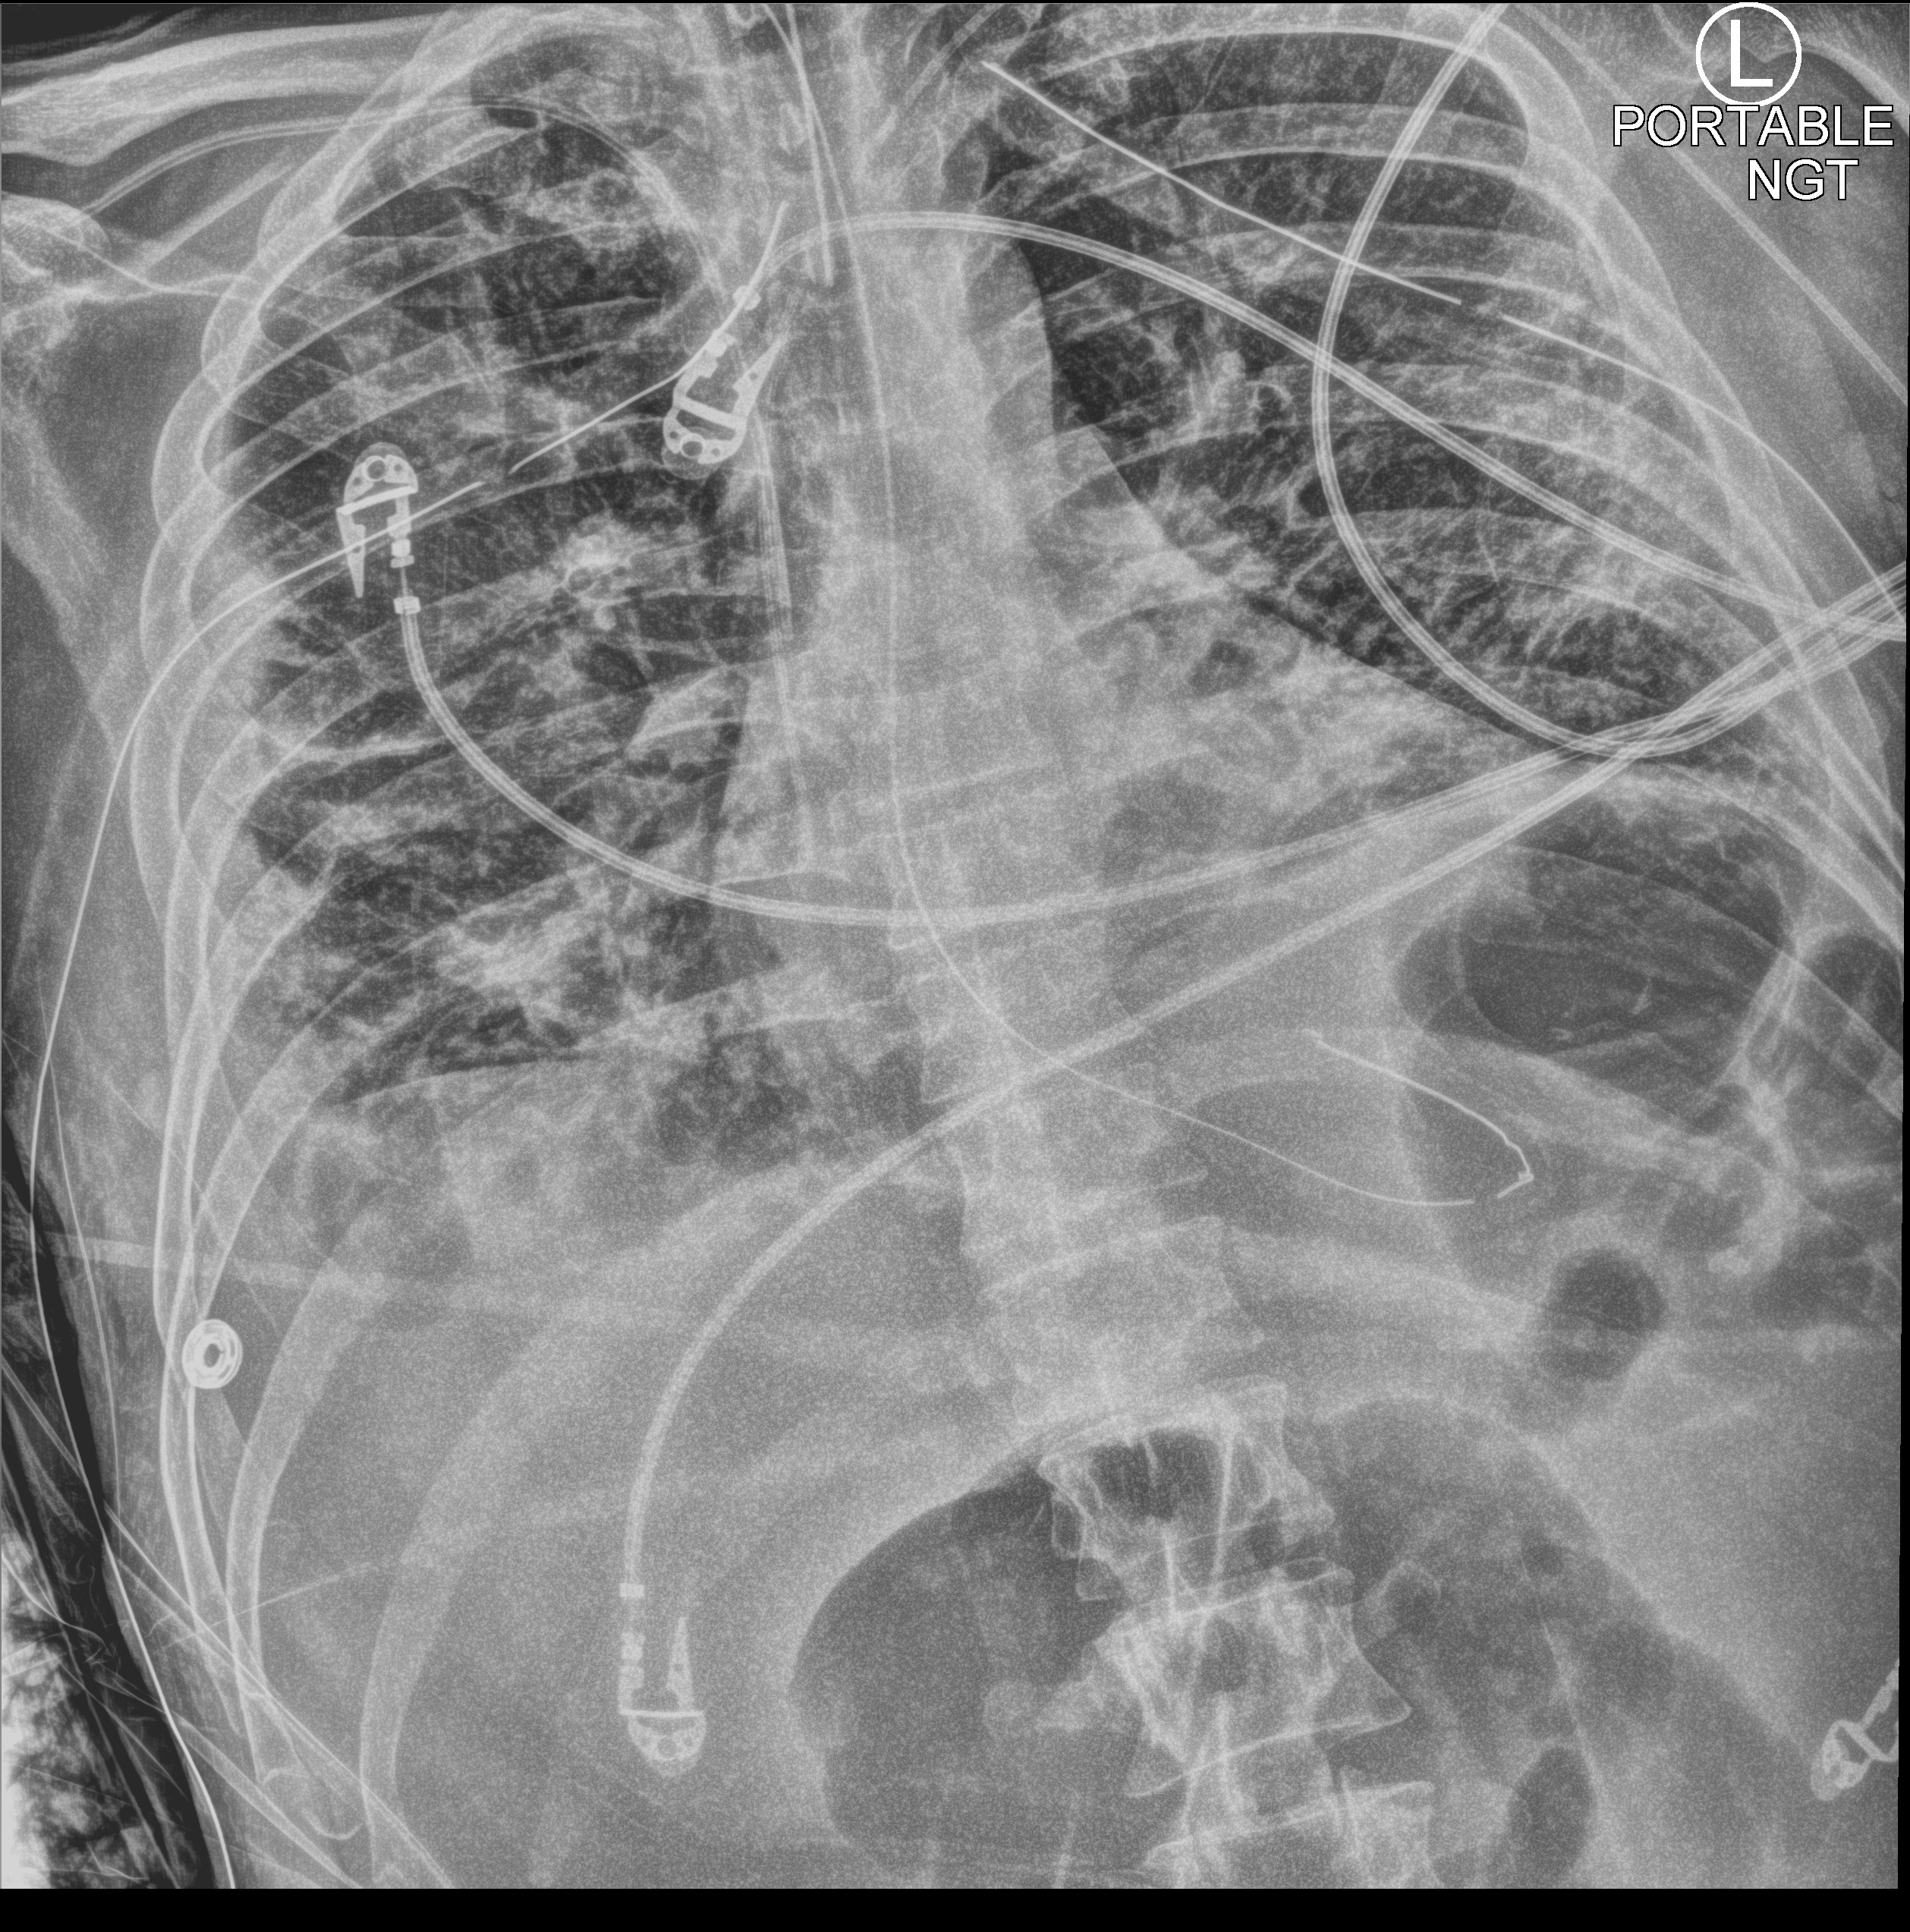
Bedside chest radiograph (computed radiography). Male patient hospitalised with COVID-19, age 18–59 years.
Hospital-stay facts (about this admission, not read from this image; timing relative to this image not recorded): length of hospital stay: 96 days; chronic kidney disease (admission record): no.